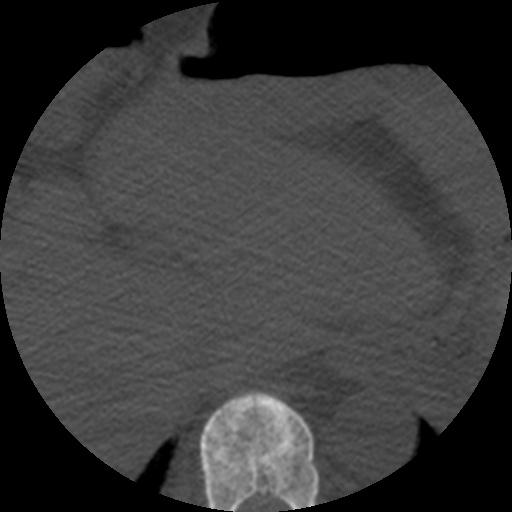
CT including the spine, one axial slice; position 265 of 508 along the scan axis; 120 kVp; bone window (W 1800 / L 400 HU); 512 × 512 image matrix. Patient age 57 years. Case-level facts recorded for this patient, not image findings: primary cancer: prostate.
Outlined on this slice (semi-automatic segmentation, software-assisted and operator-edited):
- T10 vertebra: bounding box (x1, y1, x2, y2) in pixels: (199, 390, 320, 512)